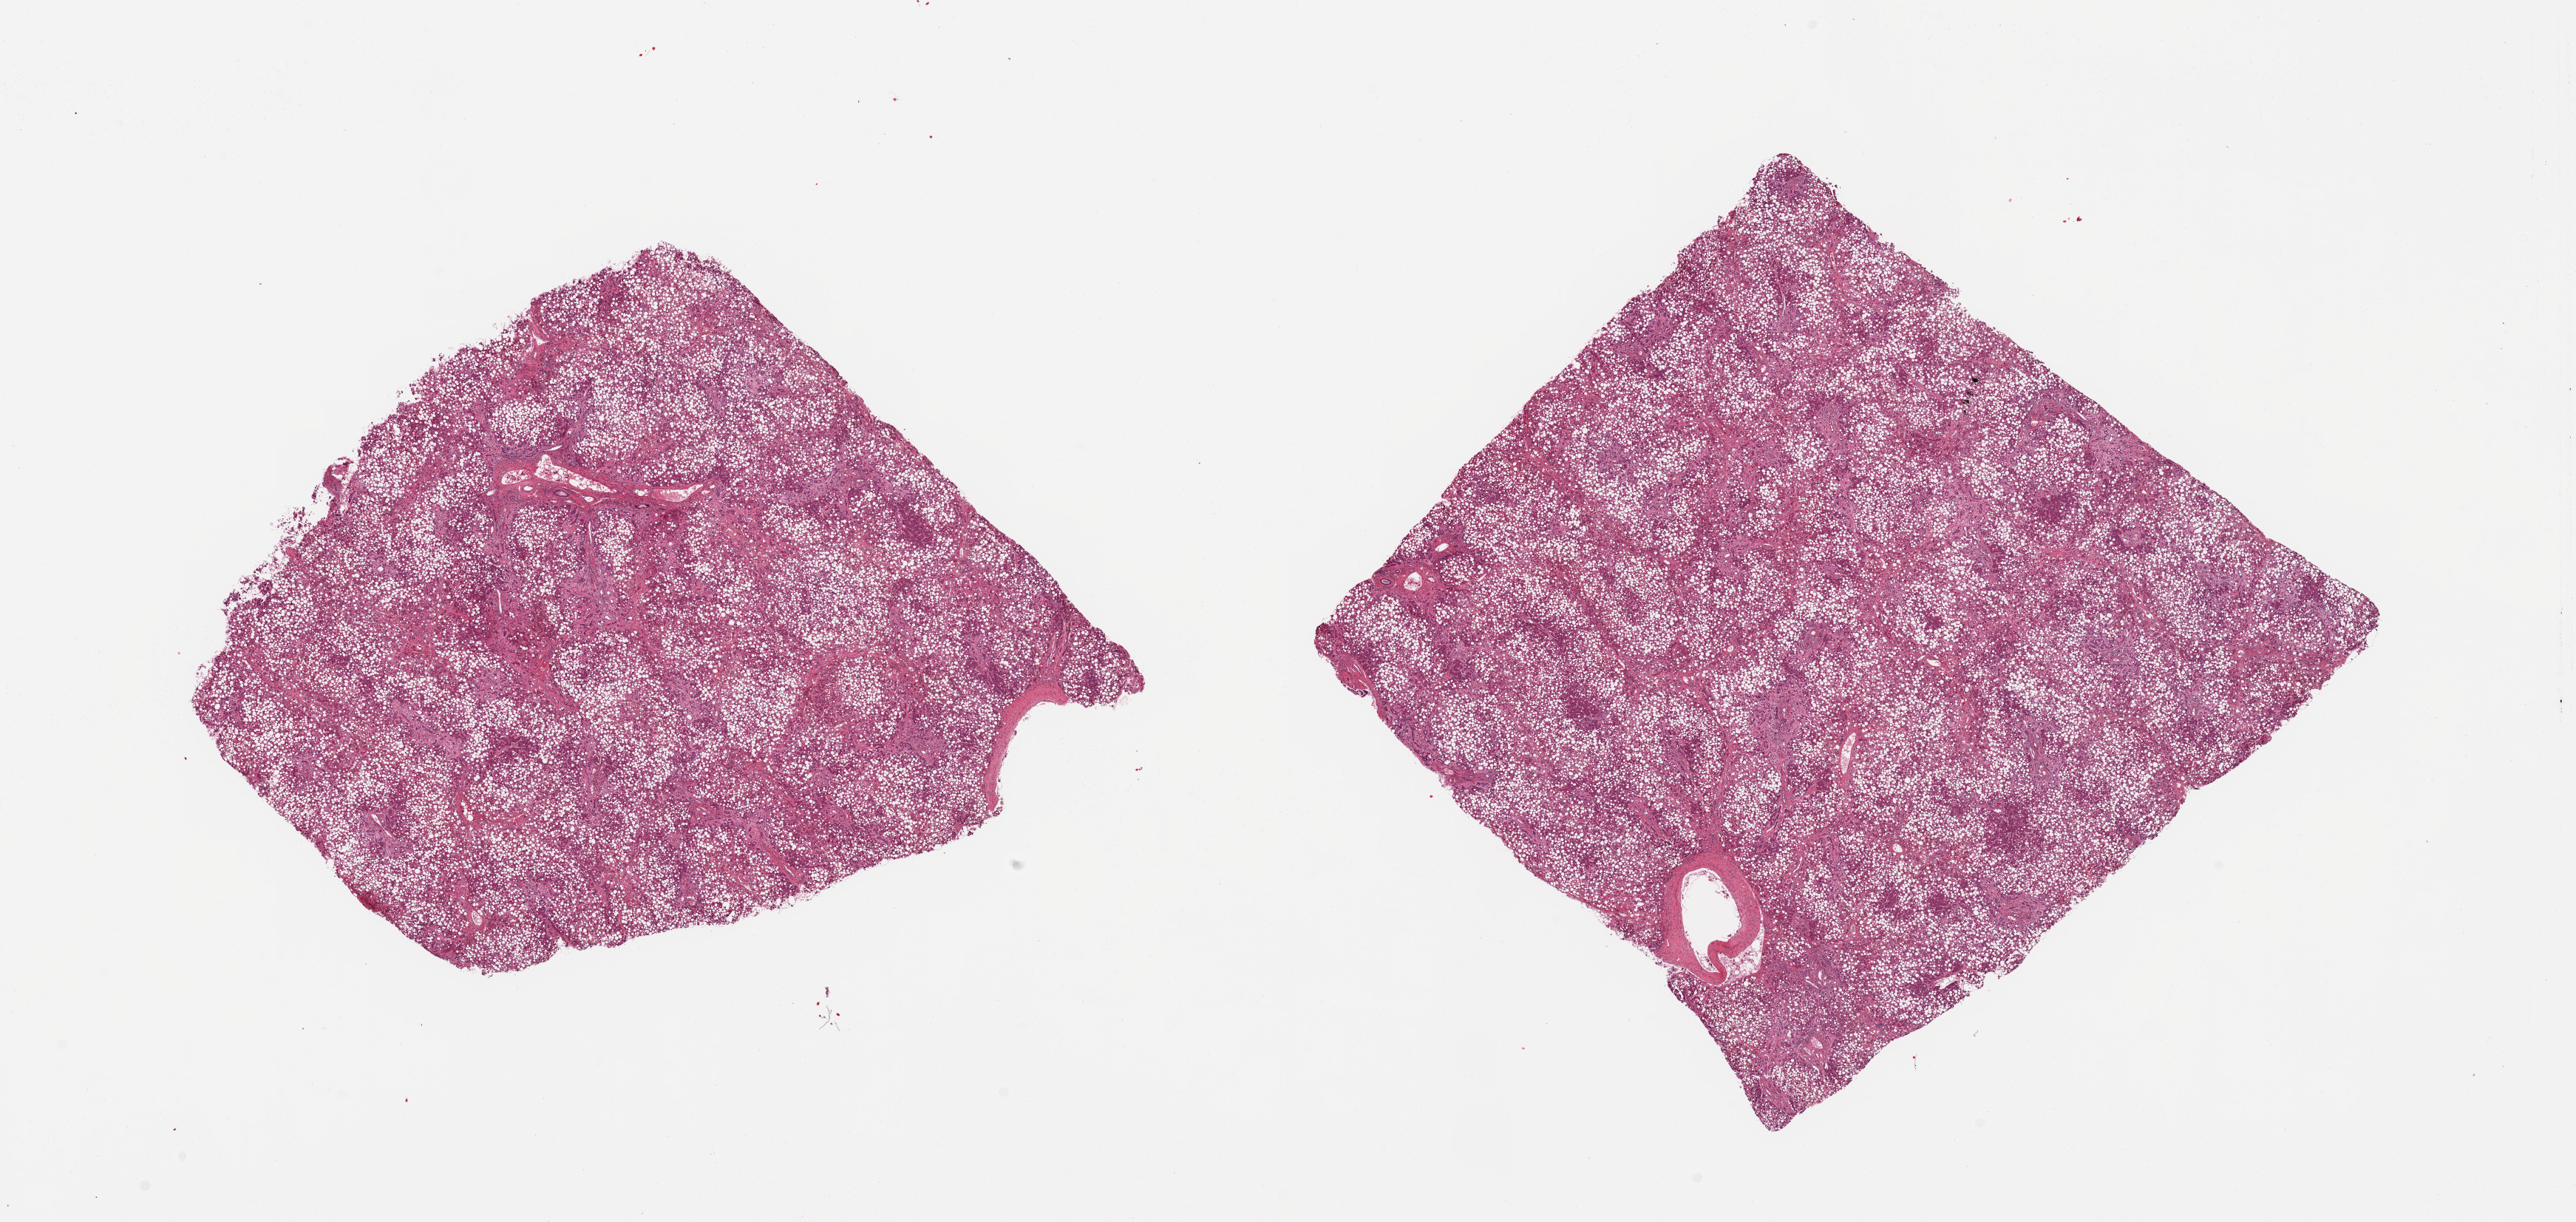
Whole-slide image, haematoxylin and eosin stain, shown as a low-resolution overview of the whole scanned area (about 27.6 x 13.1 mm, acquisition: 20x scan). PAXgene-fixed paraffin-embedded (PFPE) section. Target tissue: liver. Donor tissue sample. Donor: female.
Reviewer comment on this tissue sample: 2 pieces; many Mallory alcoholic hyalin bodies, bridging fibrosis, >90% macro and microsteatosis.